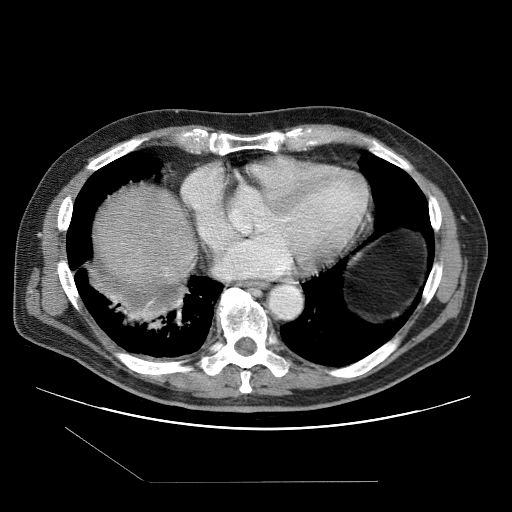
Contrast-enhanced abdominal CT (liver protocol), one axial slice. Slice 99 of 109 in the series (ordered by position). Reconstruction kernel STANDARD. 120 kVp. One of 2 acquisitions stored at this slice position. Soft-tissue window (W 400 / L 40 HU). 2.5 mm slice thickness. 512 × 512 image matrix, field of view 400 × 400 mm. From the clinical record (not read from this slice): diagnosis: hepatocellular carcinoma (patient treated with transarterial chemoembolisation; whether this scan precedes or follows treatment is not stated here); TNM stage (as recorded): Stage-IIIB; Child-Pugh class: A.
Annotated regions visible in this slice (semi-automatically segmented with operator editing):
- liver parenchyma outside the tumour (the mass and vessels are separate outlines, so this box may not span the whole liver): bounding box (x1, y1, x2, y2) in pixels: (96, 188, 196, 310)